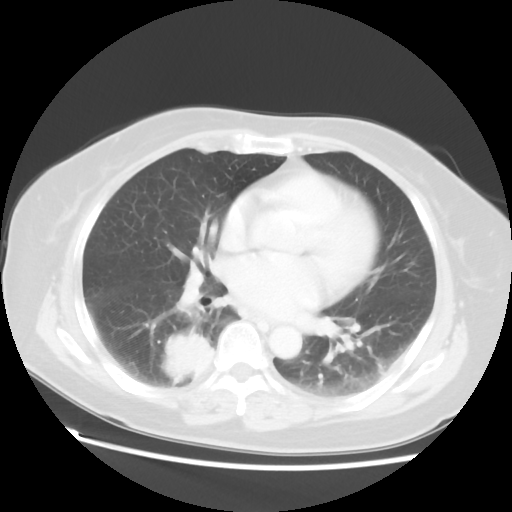
Chest CT, one axial slice. Slice 27 of 52 in the series (ordered by position). 120 kVp. Lung window (W 1500 / L -600 HU). 5 mm slice thickness. 512 × 512 image matrix. Female patient, age 69 years. Case-level facts recorded for this patient, not image findings: clinical TNM (as recorded): T2 N1 M1a.
Structures marked on this image (bounding box drawn by a radiologist):
- lung tumour (recorded histology: adenocarcinoma): bounding box [x1, y1, x2, y2] px = [163, 327, 218, 396]